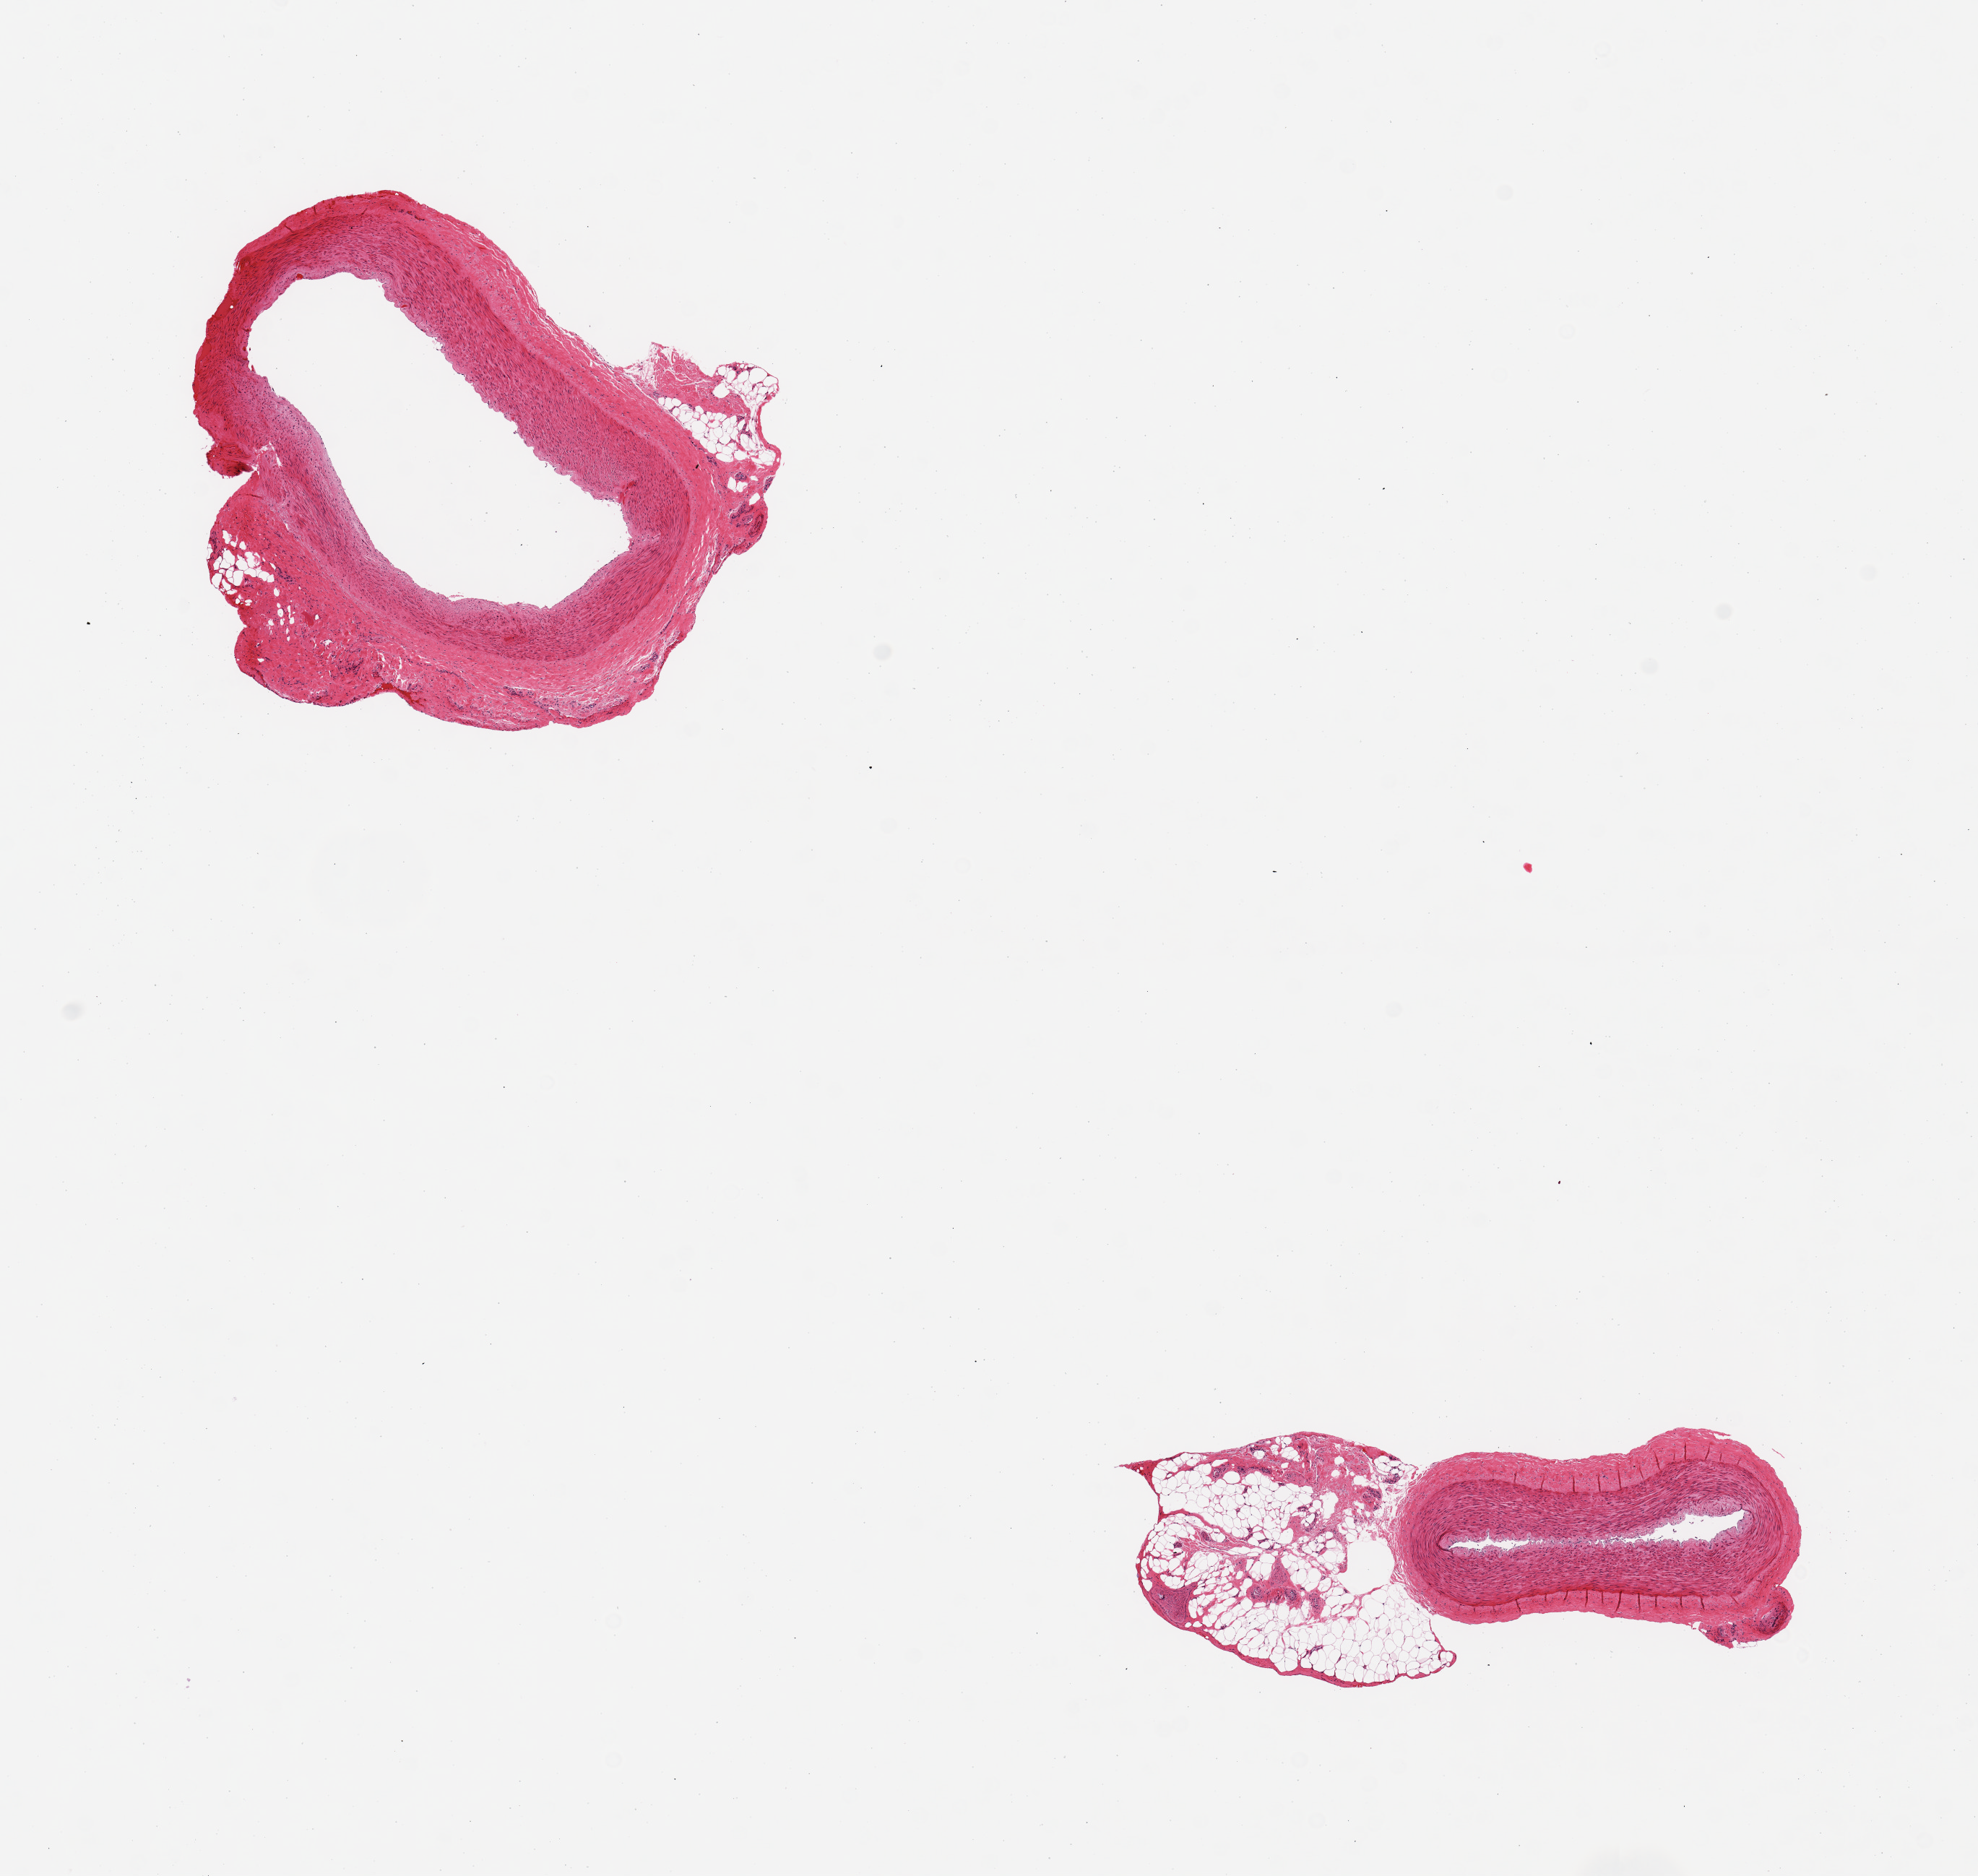
Whole-slide image, H&E stain, shown as a low-resolution overview of the whole scanned area (about 10.8 x 10.3 mm, slide scanned at 20x). PAXgene-fixed, paraffin-embedded tissue. Section of tibial artery (target tissue). Donor tissue sample. Donor sex: male.
Reviewer comment on this tissue sample: 2 pieces, adherent rims of fibrous tissue/fat up to ~1mm.